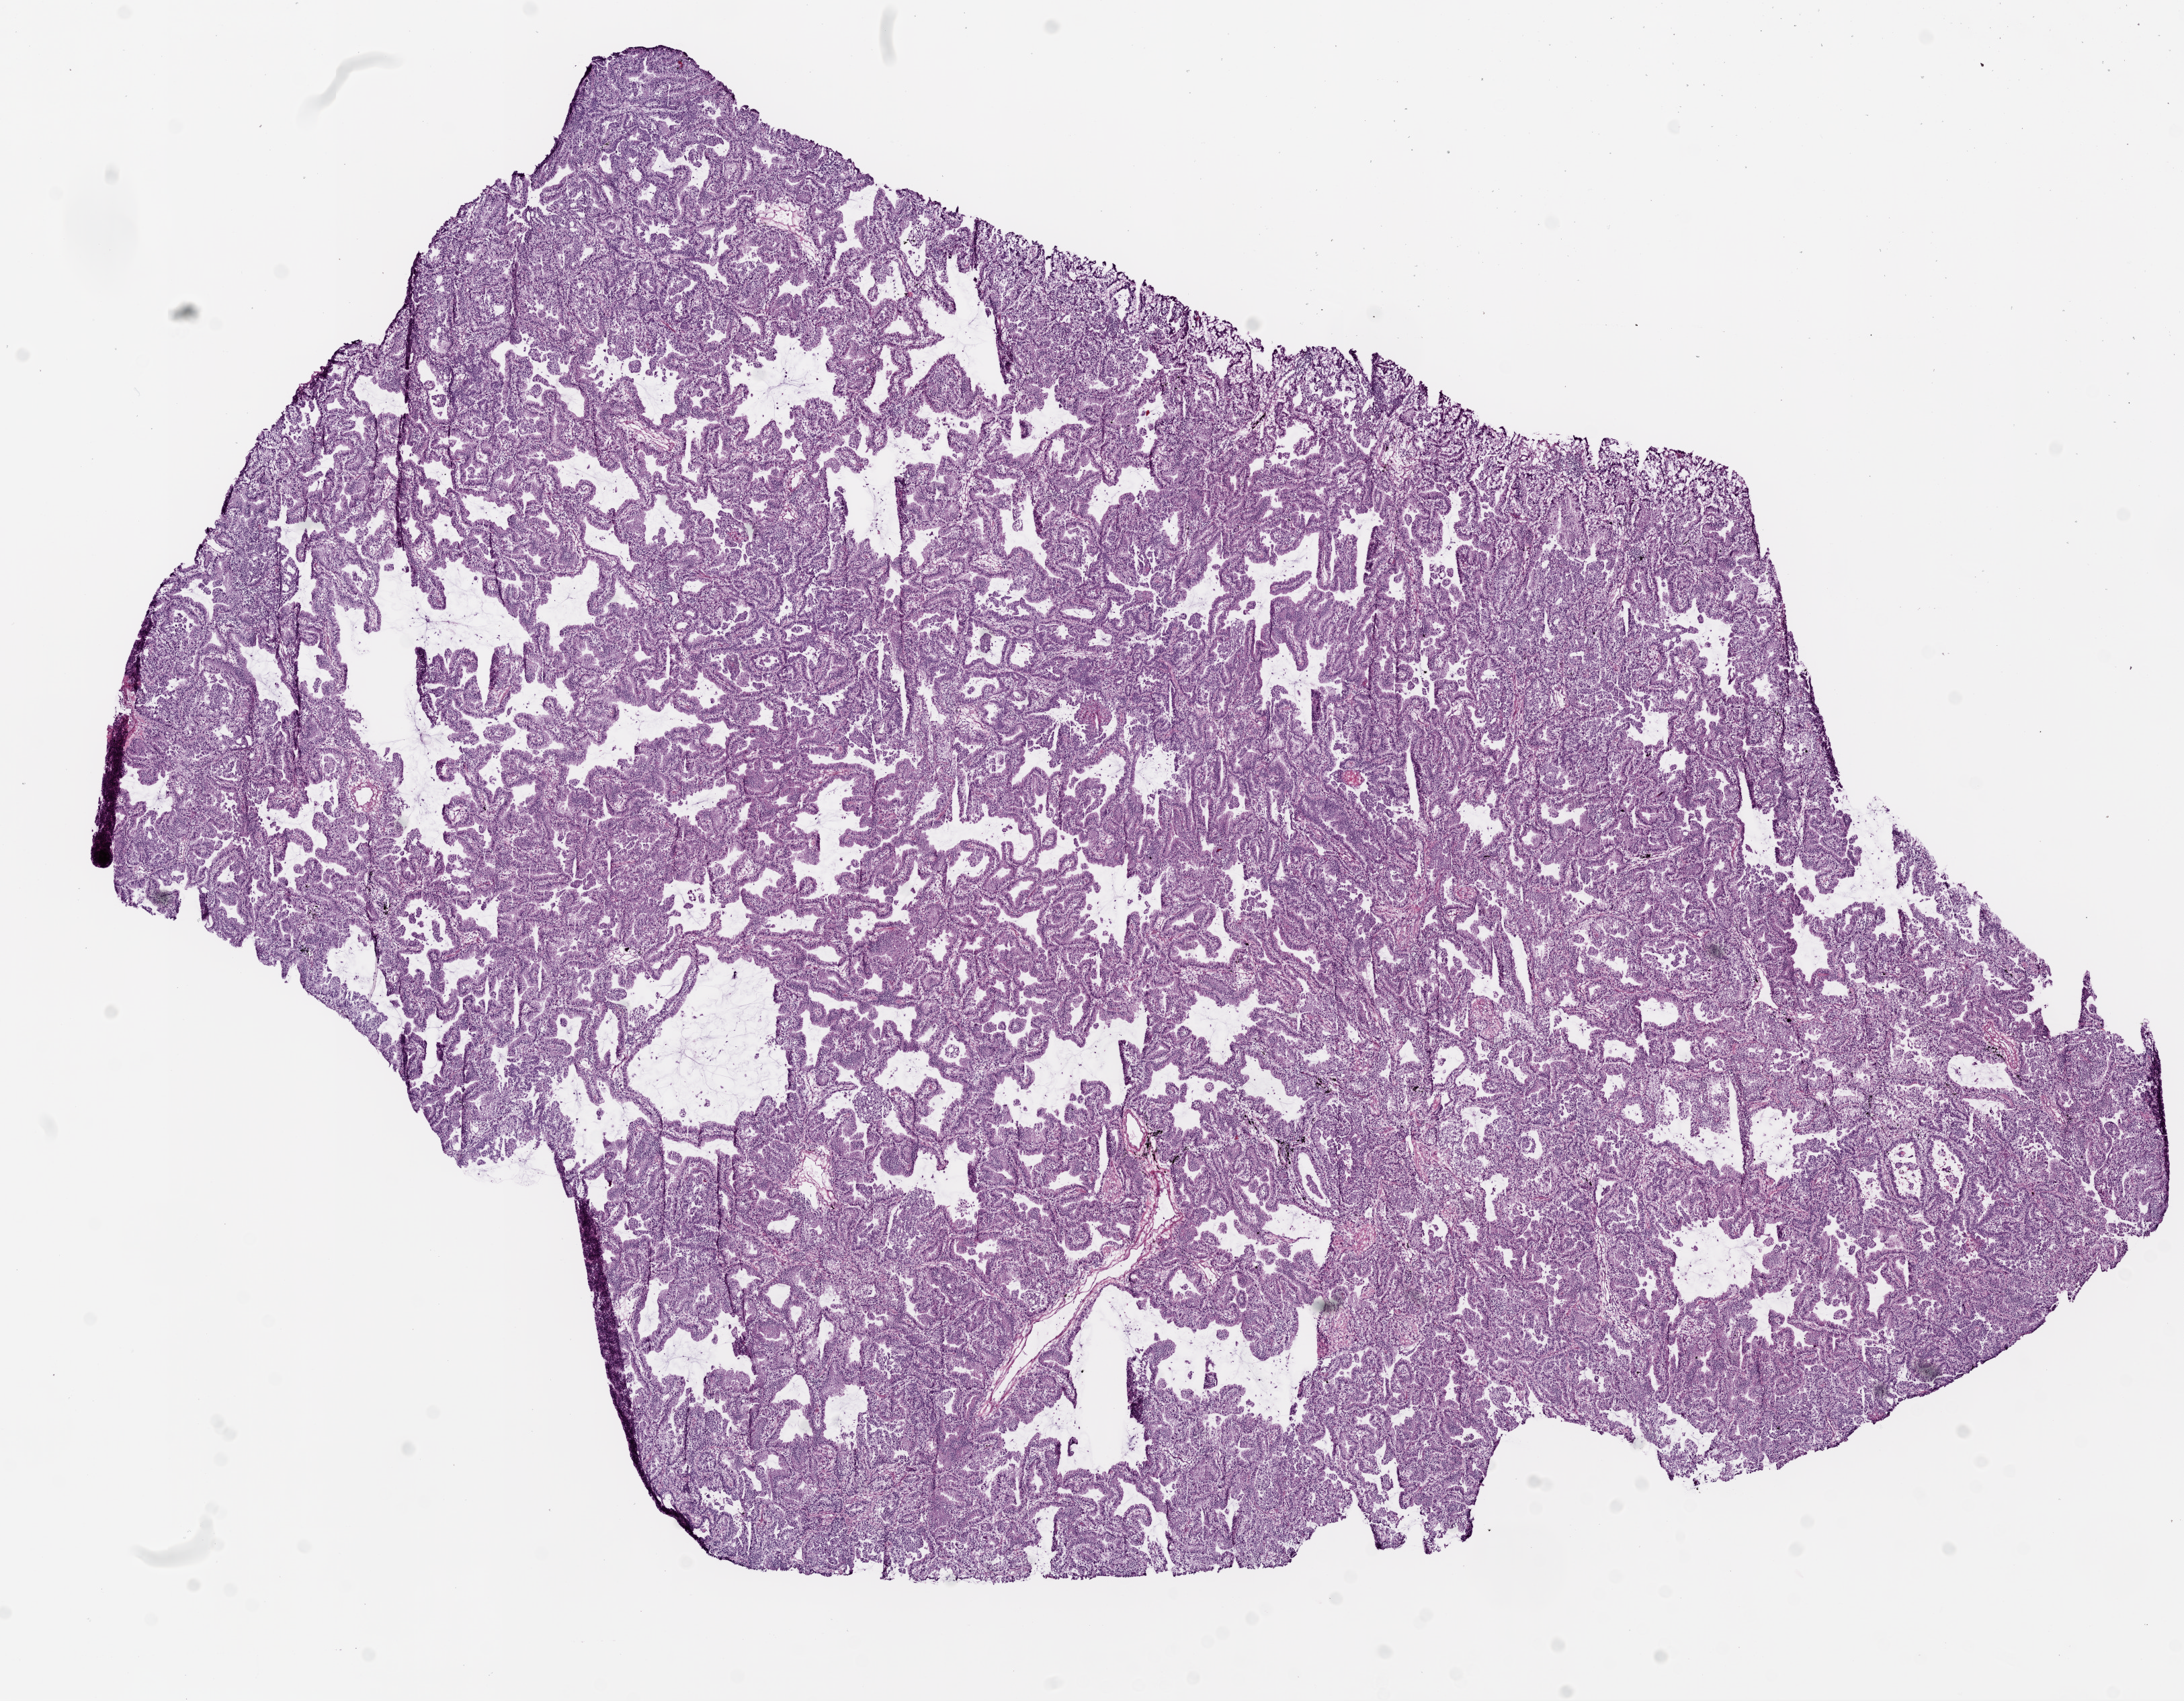
Hematoxylin and eosin (H&E) stained whole-slide image, a low-resolution overview of the entire scanned area, about 13.0 x 10.2 mm (from a 20x scan); frozen section; lung, primary tumour sample. Male patient; age at initial diagnosis 76 years. Pathologist review of this section (percent, as recorded): tumour nuclei 75%, normal cells 0%, stromal cells 10%, necrosis 0%.
AJCC pathologic stage: IIIB. Histologic diagnosis: Adenocarcinoma with mixed subtypes (lower lobe, lung). Laterality: right.